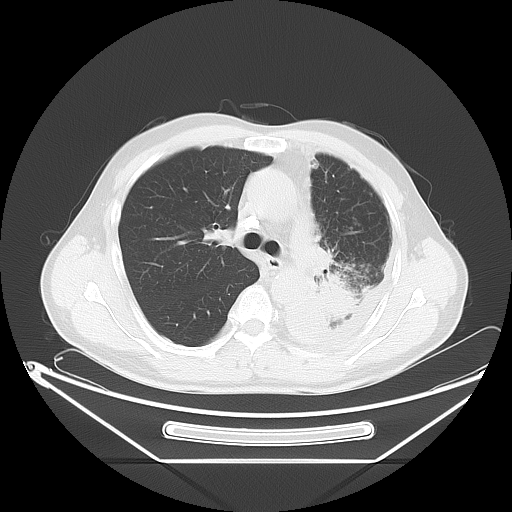
Chest CT, one axial slice. Slice 41 of 63 in the series (ordered by position). Reconstruction kernel LUNG. Lung window (W 1500 / L -600 HU). 512 × 512 image matrix, field of view 442 × 442 mm. Male patient, age 60 years. Case-level facts recorded for this patient, not image findings: clinical TNM (as recorded): T4 N1 M1.
Annotated regions visible in this slice (rectangle marked by the reading radiologist):
- lung tumour (recorded histology: adenocarcinoma): bounding box [x1, y1, x2, y2] px = [307, 273, 363, 336]